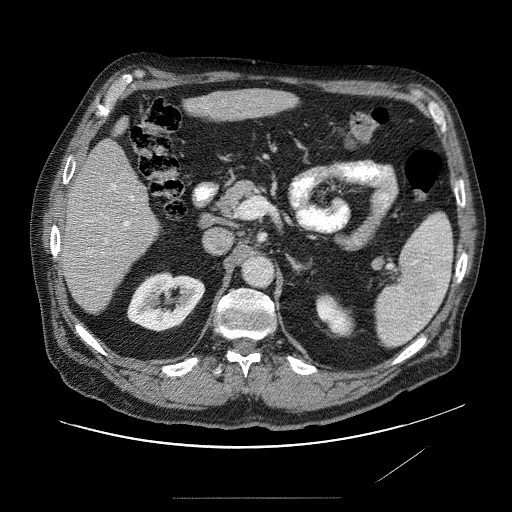
Contrast-enhanced abdominal CT (liver protocol), one axial slice. Slice 33 of 89 in the series (ordered by position). Soft-tissue window (W 400 / L 40 HU). 2.5 mm slice thickness. 512 × 512 image matrix. From the clinical record (not read from this slice): diagnosis: hepatocellular carcinoma (patient treated with transarterial chemoembolisation; whether this scan precedes or follows treatment is not stated here); TNM stage (as recorded): Stage-IVA; Child-Pugh class: A; tumour differentiation: moderately differentiated.
Outlined on this slice (semi-automatic segmentation, software-assisted and operator-edited):
- liver parenchyma outside the tumour (the mass and vessels are separate outlines, so this box may not span the whole liver): bounding box (x1, y1, x2, y2) in pixels: (62, 86, 304, 314)
- mass: (184, 96, 205, 121)
- liver vessels: (102, 111, 214, 283)